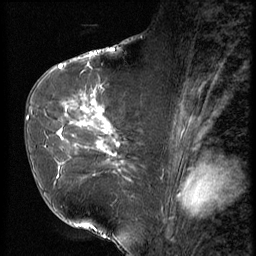
Breast MRI (dynamic contrast-enhanced), one sagittal slice. Slice 36 of 56 in the series (ordered by position). 3 images stored at this slice position (order not interpretable as contrast timing). 1.5 T. TE 4.2 ms, TR 9 ms. 256 × 256 image matrix, field of view 180 × 180 mm. Female patient, age 61 years. Case-level facts recorded for this patient, not image findings: setting: breast cancer imaged before/during neoadjuvant chemotherapy; receptor status: HR-positive, HER2-negative.
Outlined on this slice (semi-automatically segmented with operator editing):
- analysis volume of interest (the breast-tissue region the enhancement analysis was run in; not a lesion): bounding box [x1, y1, x2, y2] px = [47, 89, 153, 191]
- tumour enhancement mask (voxels above the 140 % enhancement threshold inside the analysis volume of interest): [56, 103, 118, 164]